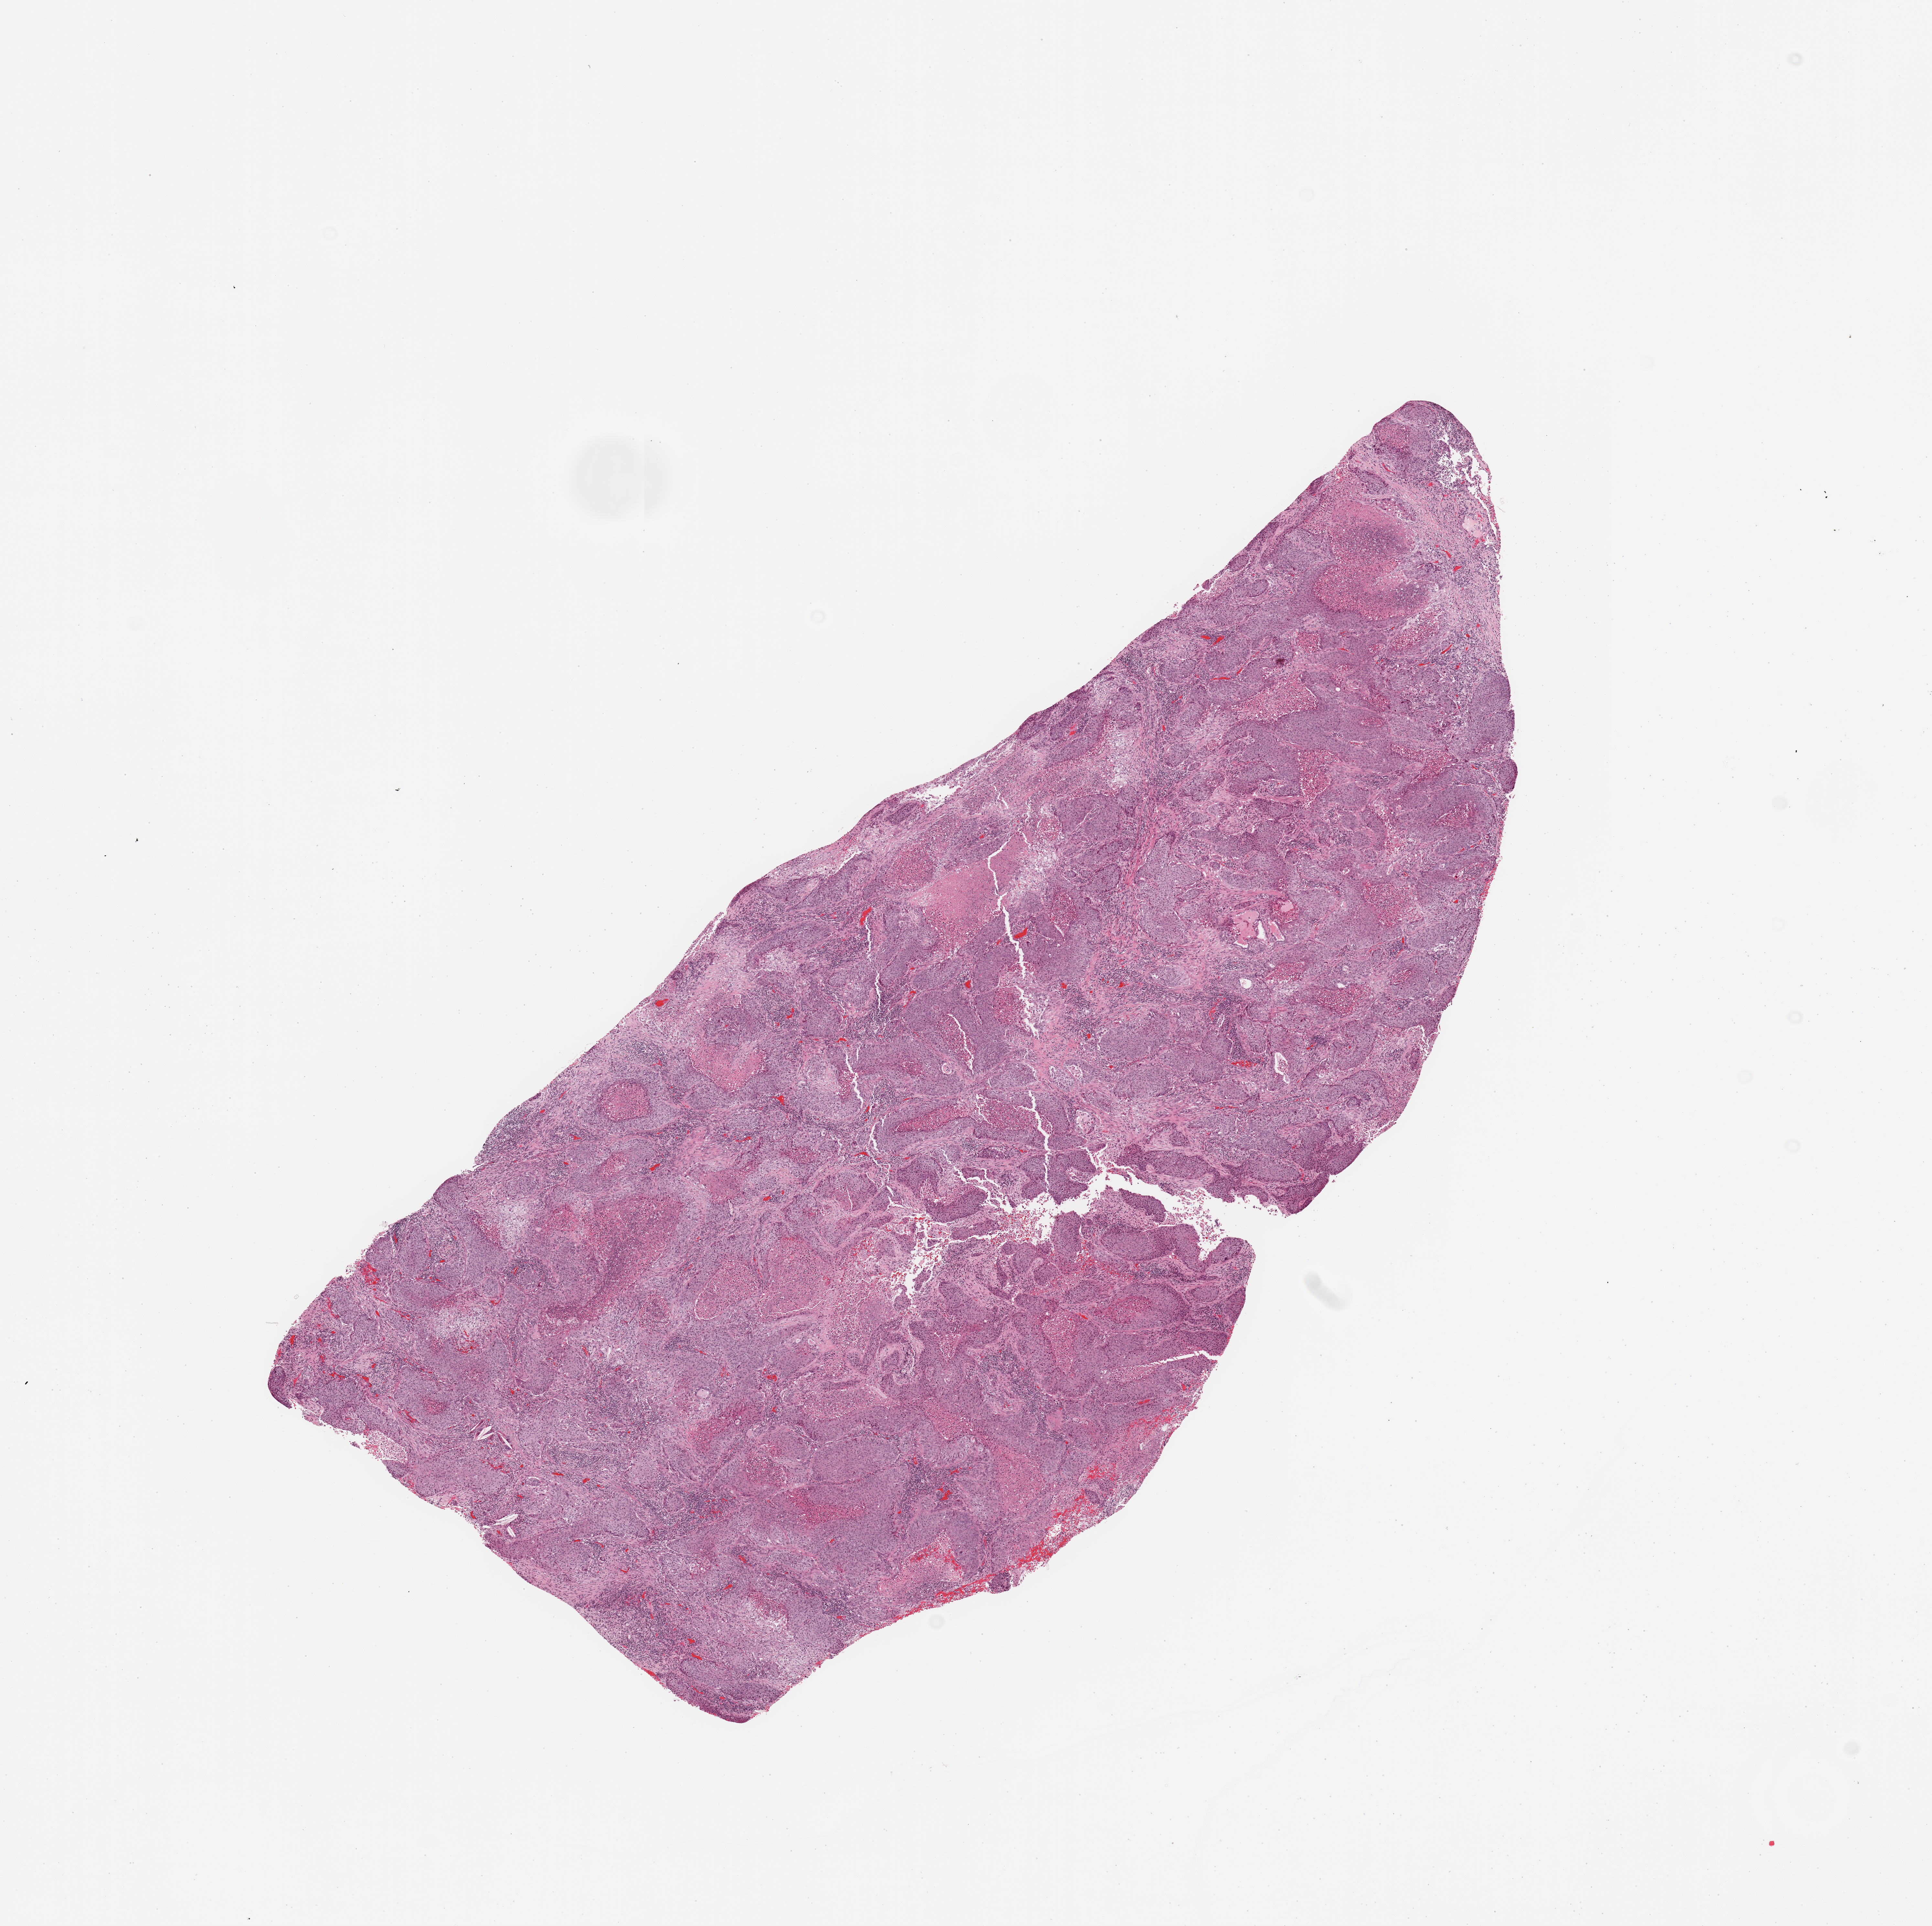
Digitized Hematoxylin and eosin (H&E) stained tissue section (whole slide), low-resolution overview of the scanned area, about 11.8 x 11.8 mm (from a 20x scan); tumour tissue sample, sampled site: lung. Patient: female, age 74 years. Composition of this section per pathologist review: tumour nuclei 70%, necrosis 20%.
Histologic diagnosis: Squamous cell carcinoma, NOS.